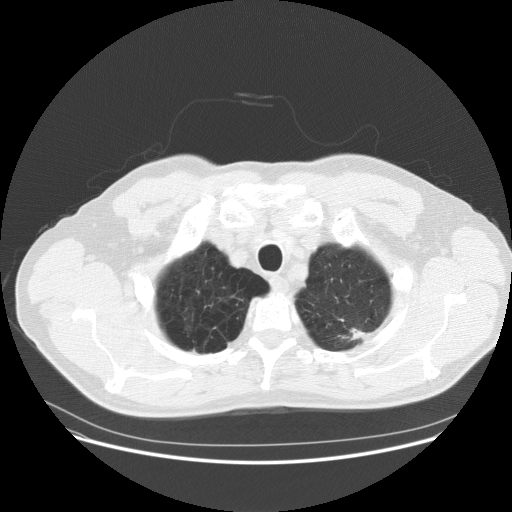
Low-dose screening chest CT, one axial slice. Slice 146 of 158 in the series (ordered by position). Reconstruction kernel STANDARD. 120 kVp. Lung window (W 1500 / L -600 HU). 512 × 512 image matrix, field of view 400 × 400 mm.
Outlined on this slice (manually delineated by an expert):
- lesion 1 (tumor, upper lobe of left lung): bounding box (x1, y1, x2, y2) in pixels: (350, 328, 370, 341)